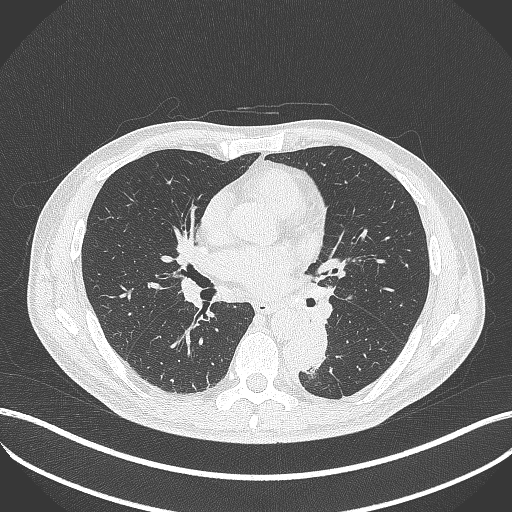
Chest CT, one axial slice. Position 209 of 451 along the scan axis. Reconstruction kernel B70f. Lung window (W 1500 / L -600 HU). 512 × 512 image matrix. Male patient, age 72 years. Case-level facts recorded for this patient, not image findings: clinical TNM (as recorded): T2b N0 M1.
Structures marked on this image (rectangle marked by the reading radiologist):
- lung tumour (recorded histology: adenocarcinoma): bounding box <285,317,327,381> (left, top, right, bottom; pixels)